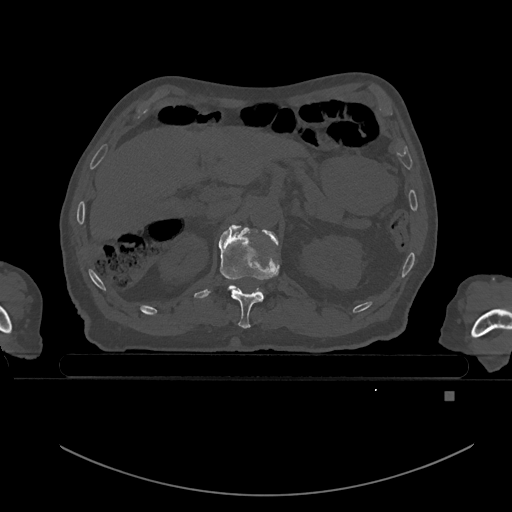
CT including the spine, one axial slice; position 9 of 969 along the scan axis; bone window (W 1800 / L 400 HU); 512 × 512 image matrix. Patient: male, 82 years. From the clinical record (not read from this slice): primary cancer: prostate; vertebrae with lytic lesions (as recorded): T11, T9, T8, T2.
Structures marked on this image (semi-automatically segmented with operator editing):
- T11 vertebra: box from (x=219, y=227) to (x=280, y=329) px